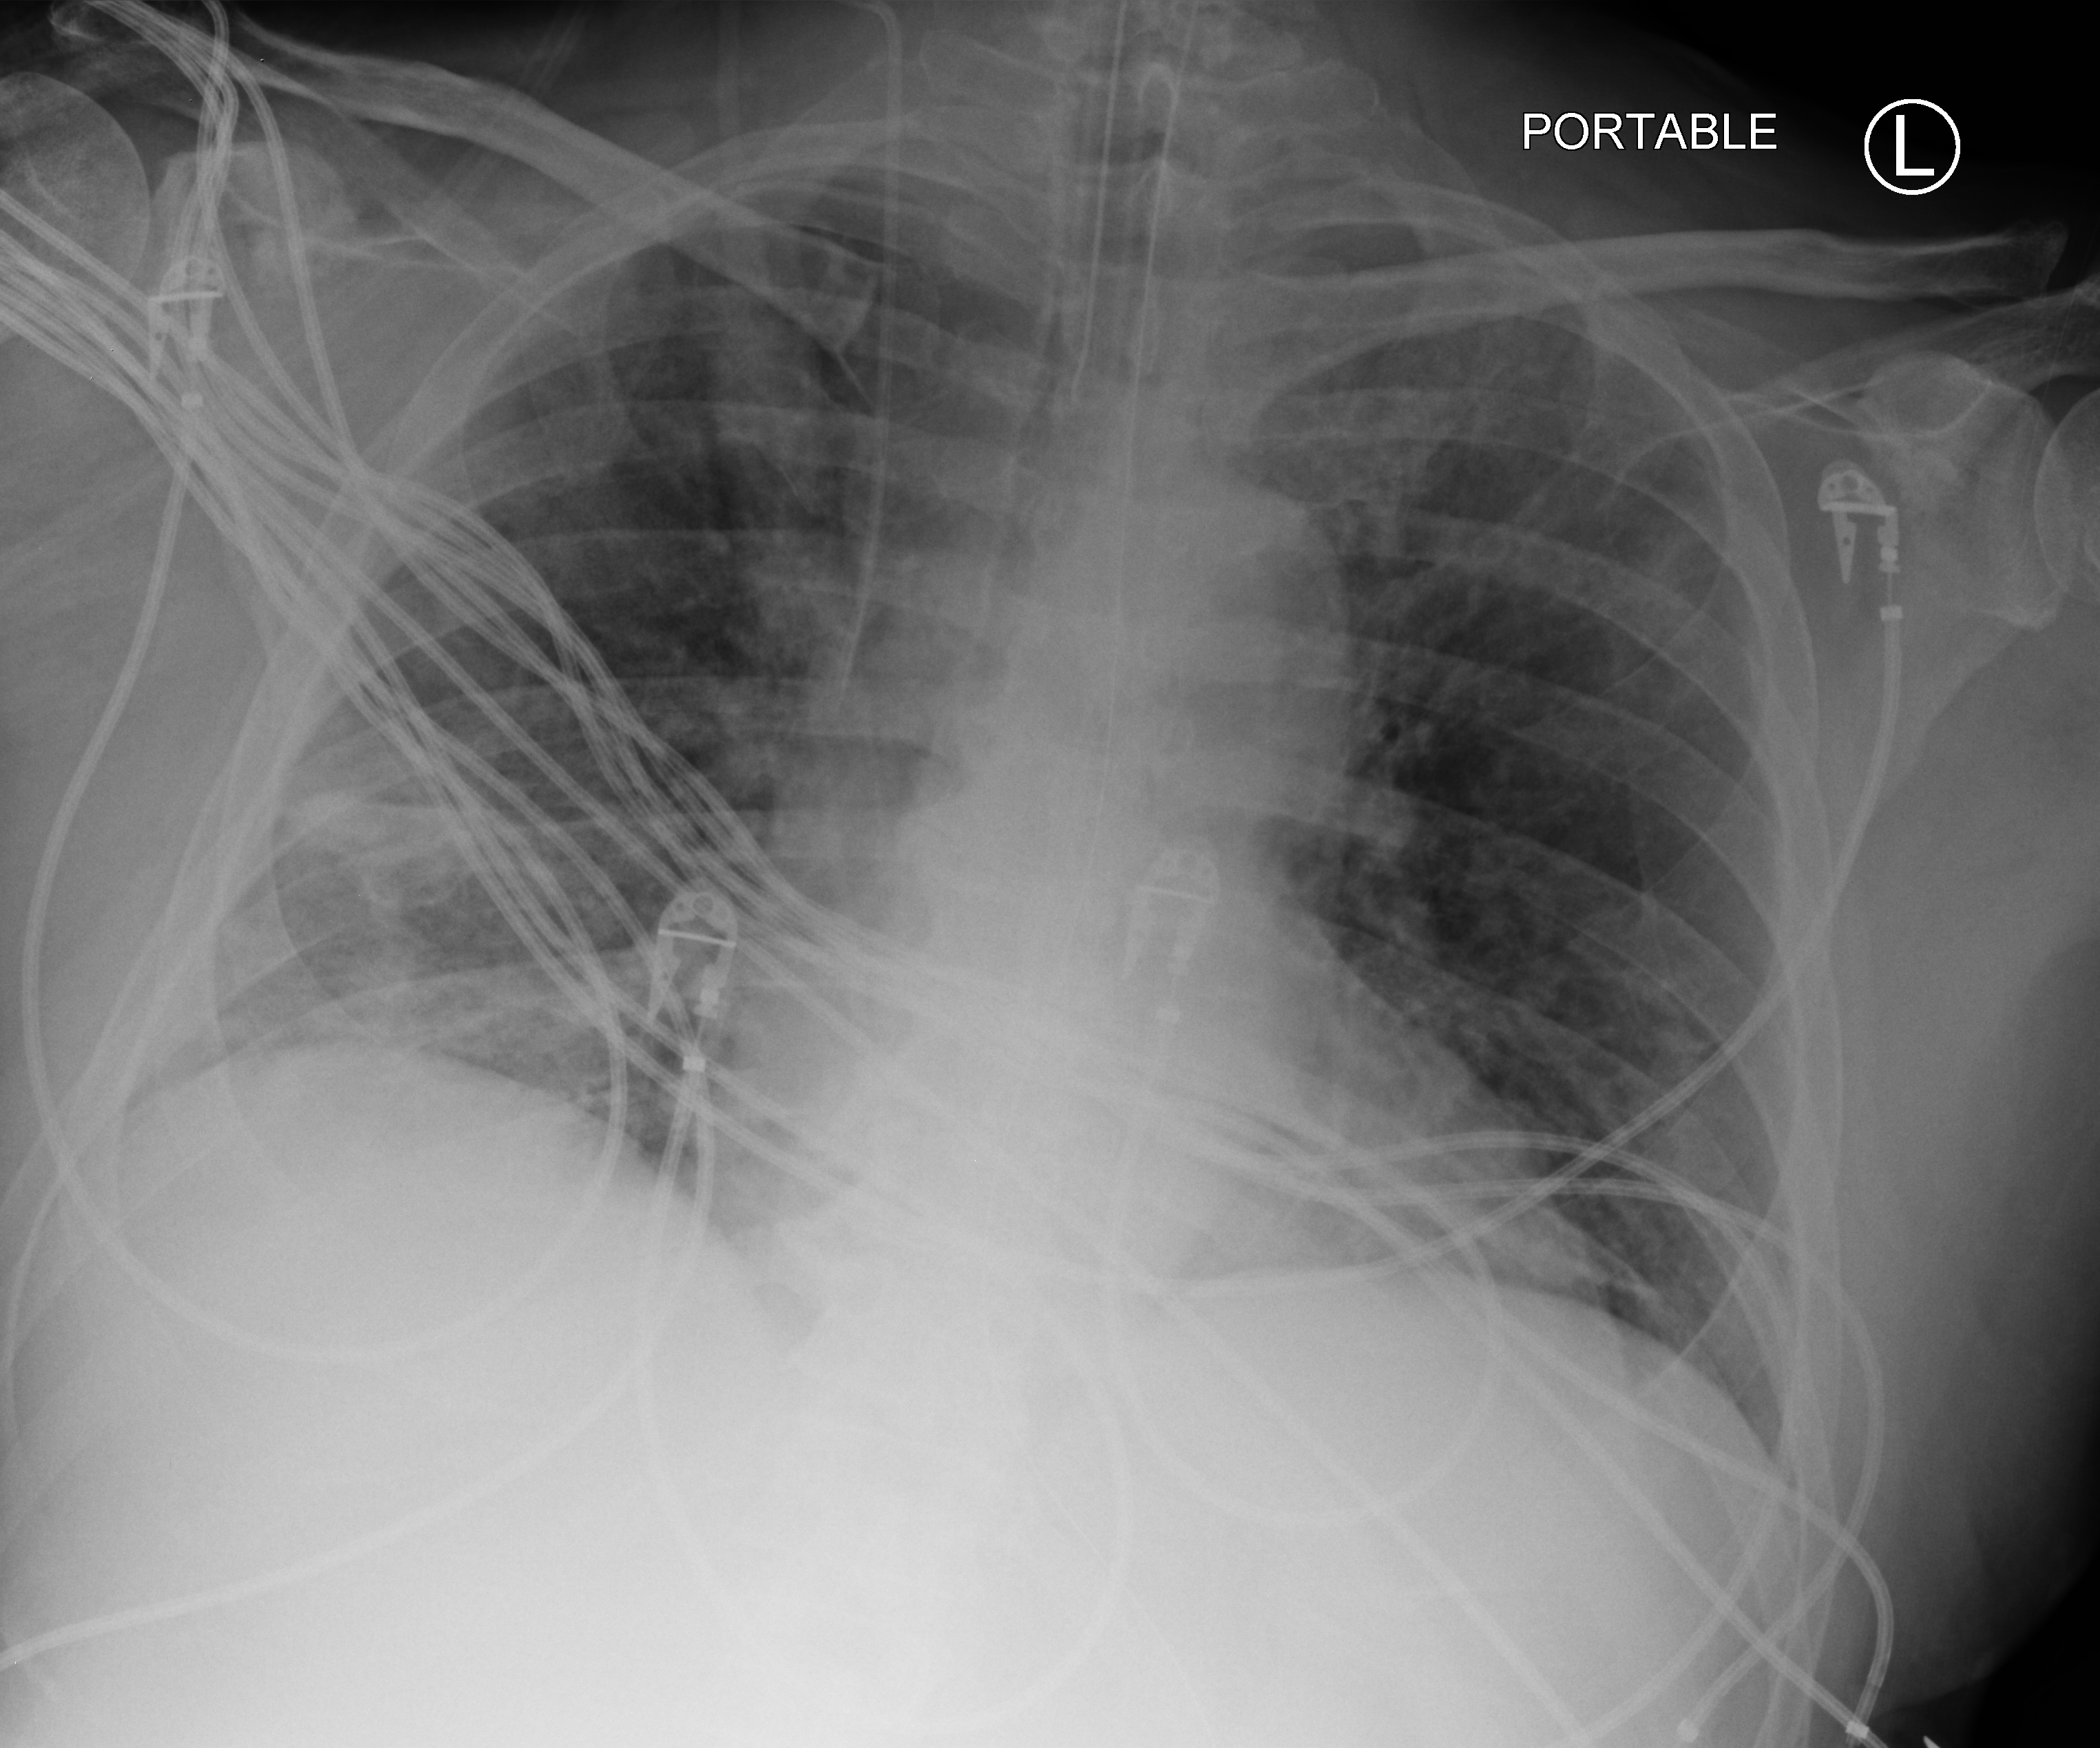
Portable chest radiograph; anteroposterior (AP) projection. Patient hospitalised with COVID-19; male, aged 60–74 years.
From the hospital-stay record, not from the radiograph (when in the stay this image was taken is not recorded): chronic kidney disease (admission record): no.